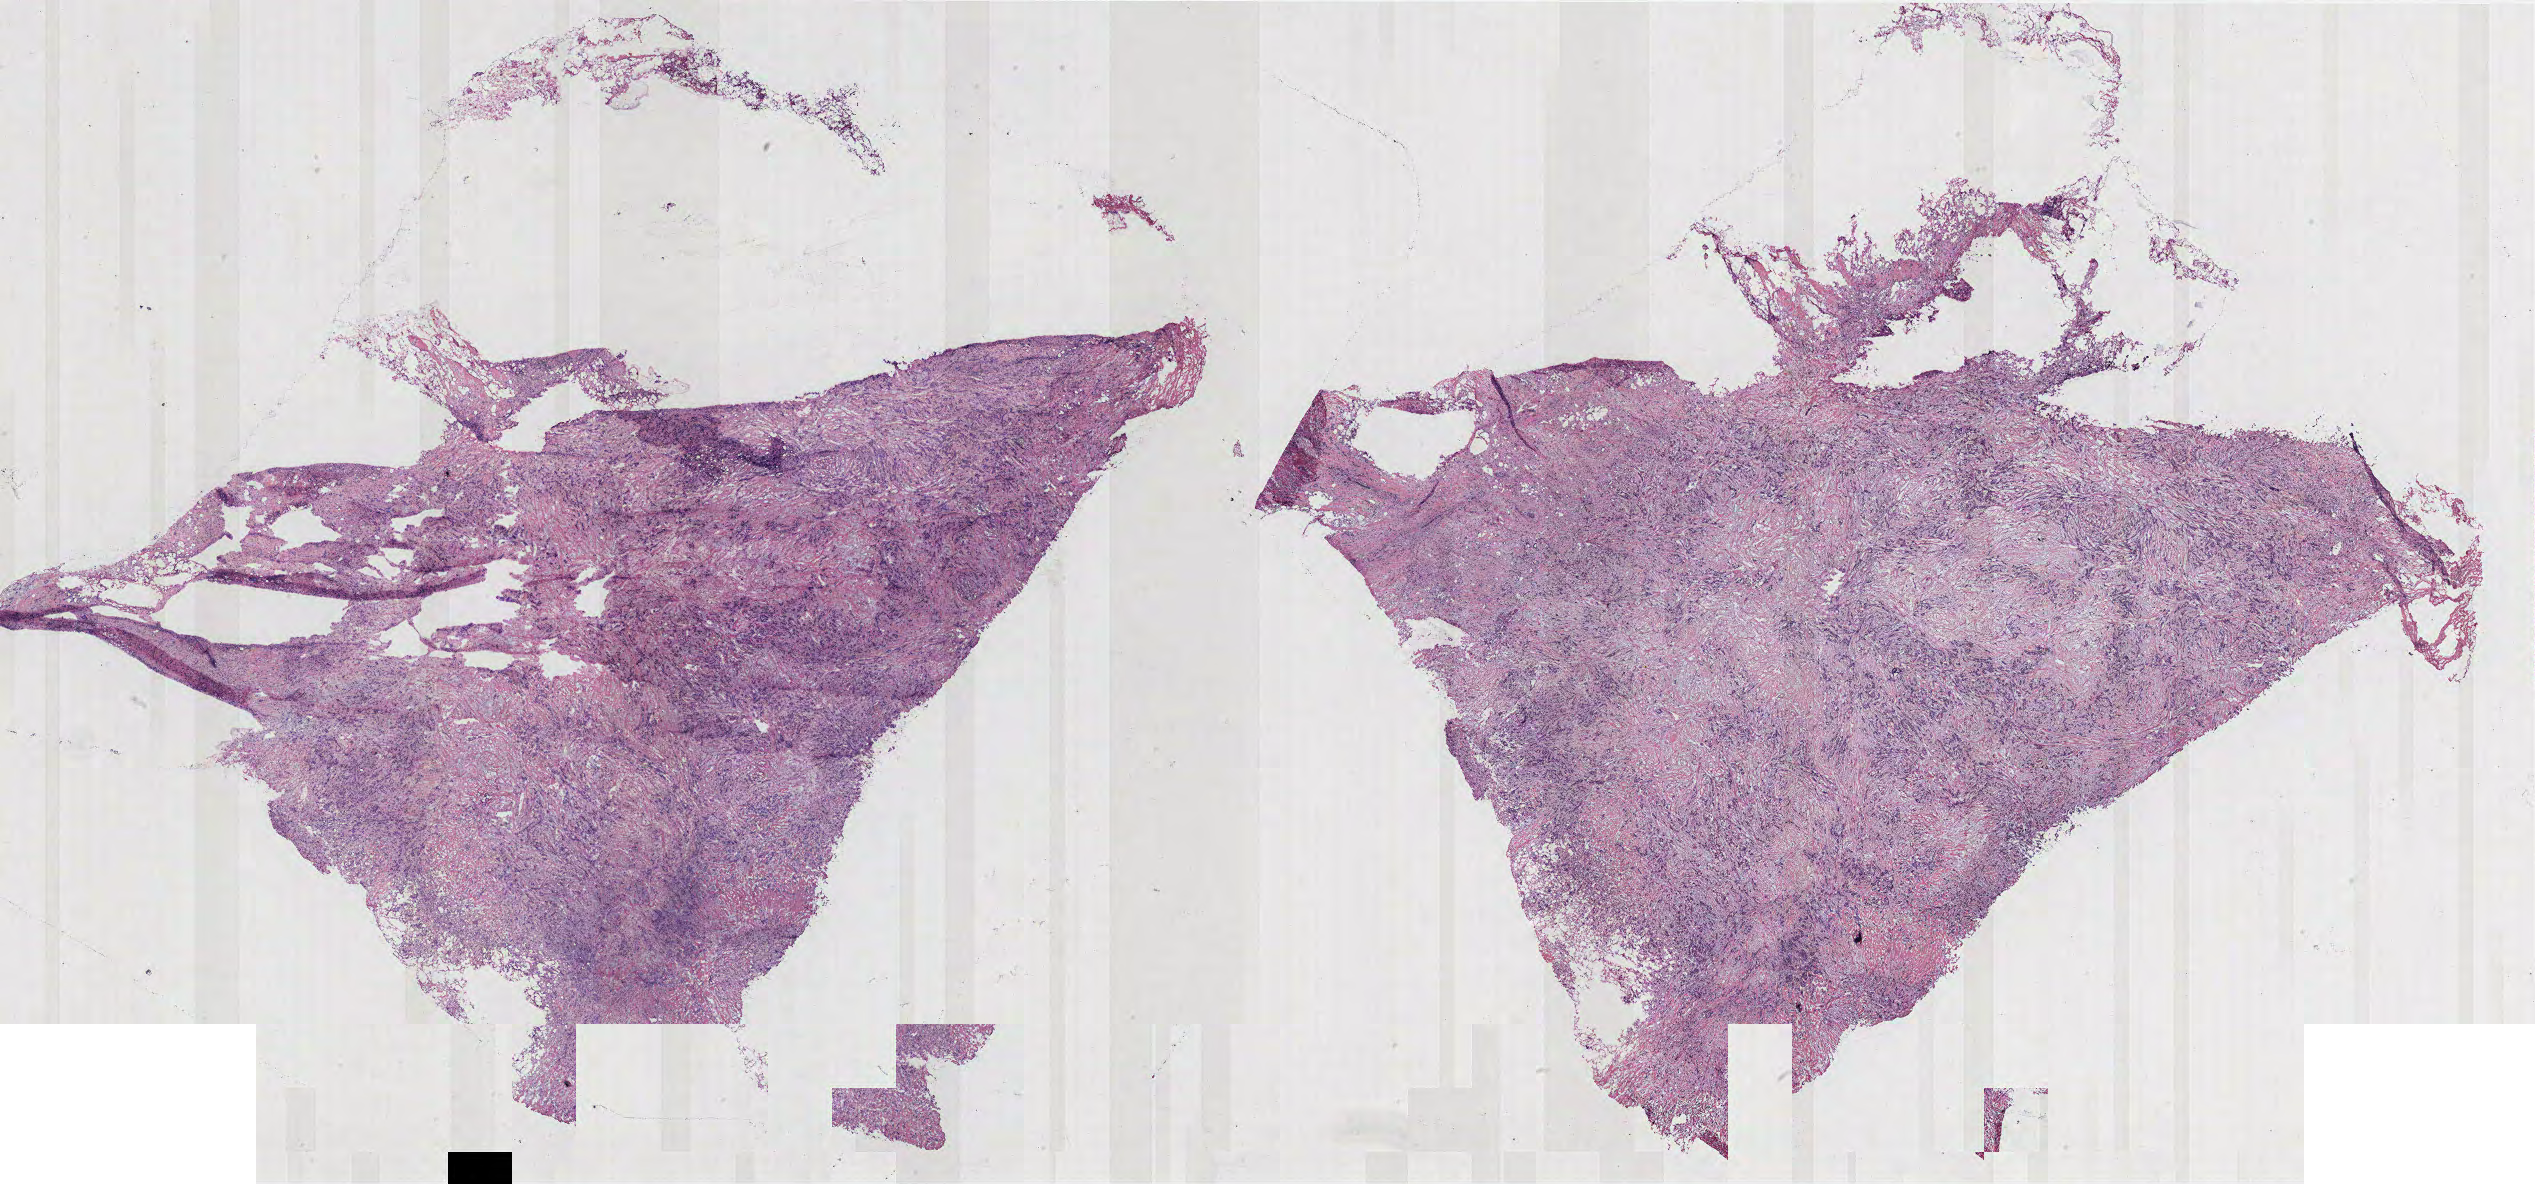
Digitized Hematoxylin and eosin (H&E) stained tissue section (whole slide), whole scanned area (about 40.6 x 19.0 mm, from a 40x scan) shown as a low-resolution overview. Breast, tissue type not recorded. Patient: female, age 56 years.
Patient diagnosis: Infiltrating duct carcinoma, NOS.